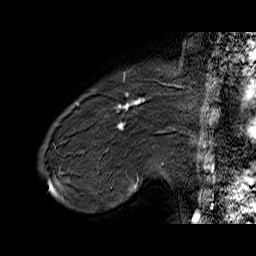
Breast MRI (dynamic contrast-enhanced), one sagittal slice. Slice 12 of 60 in the series (ordered by position). Dynamic contrast-enhanced series, time point 2 of 6 at this slice position (early post-contrast). 1.5 T. TE 6.4 ms, TR 32.9 ms. 4 mm slice thickness. 256 × 256 image matrix, field of view 200 × 200 mm. Female patient. Case-level facts recorded for this patient, not image findings: setting: breast cancer imaged before/during neoadjuvant chemotherapy; receptor status: HER2-positive.
Structures marked on this image (semi-automatic segmentation, software-assisted and operator-edited):
- analysis volume of interest (the breast-tissue region the enhancement analysis was run in; not a lesion): bounding box <71,80,155,146> (left, top, right, bottom; pixels)
- tumour enhancement mask (voxels above the 100 % enhancement threshold inside the analysis volume of interest): <117,98,144,126>